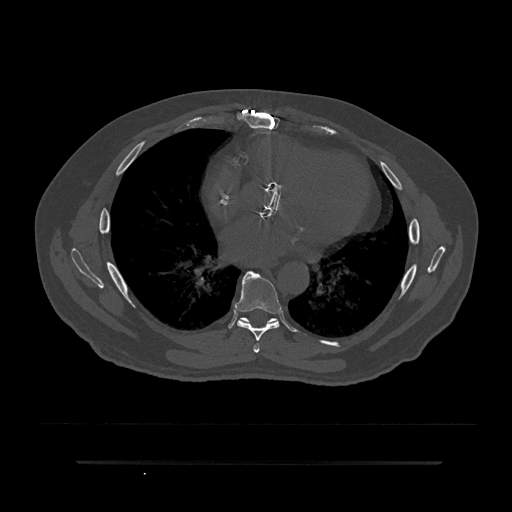
CT including the spine, one axial slice. Position 467 of 797 along the scan axis. 120 kVp. Bone window (W 1800 / L 400 HU). 0.5 mm slice thickness. 512 × 512 image matrix, field of view 464 × 464 mm. Patient: male, 59 years. From the clinical record (not read from this slice): primary cancer: bile ducts; vertebrae with lytic lesions (as recorded): T10.
Structures marked on this image (semi-automatically segmented with operator editing):
- T6 vertebra: bounding box [x1, y1, x2, y2] px = [253, 344, 260, 353]
- T7 vertebra: [234, 271, 282, 341]
- T8 vertebra: [235, 311, 295, 332]